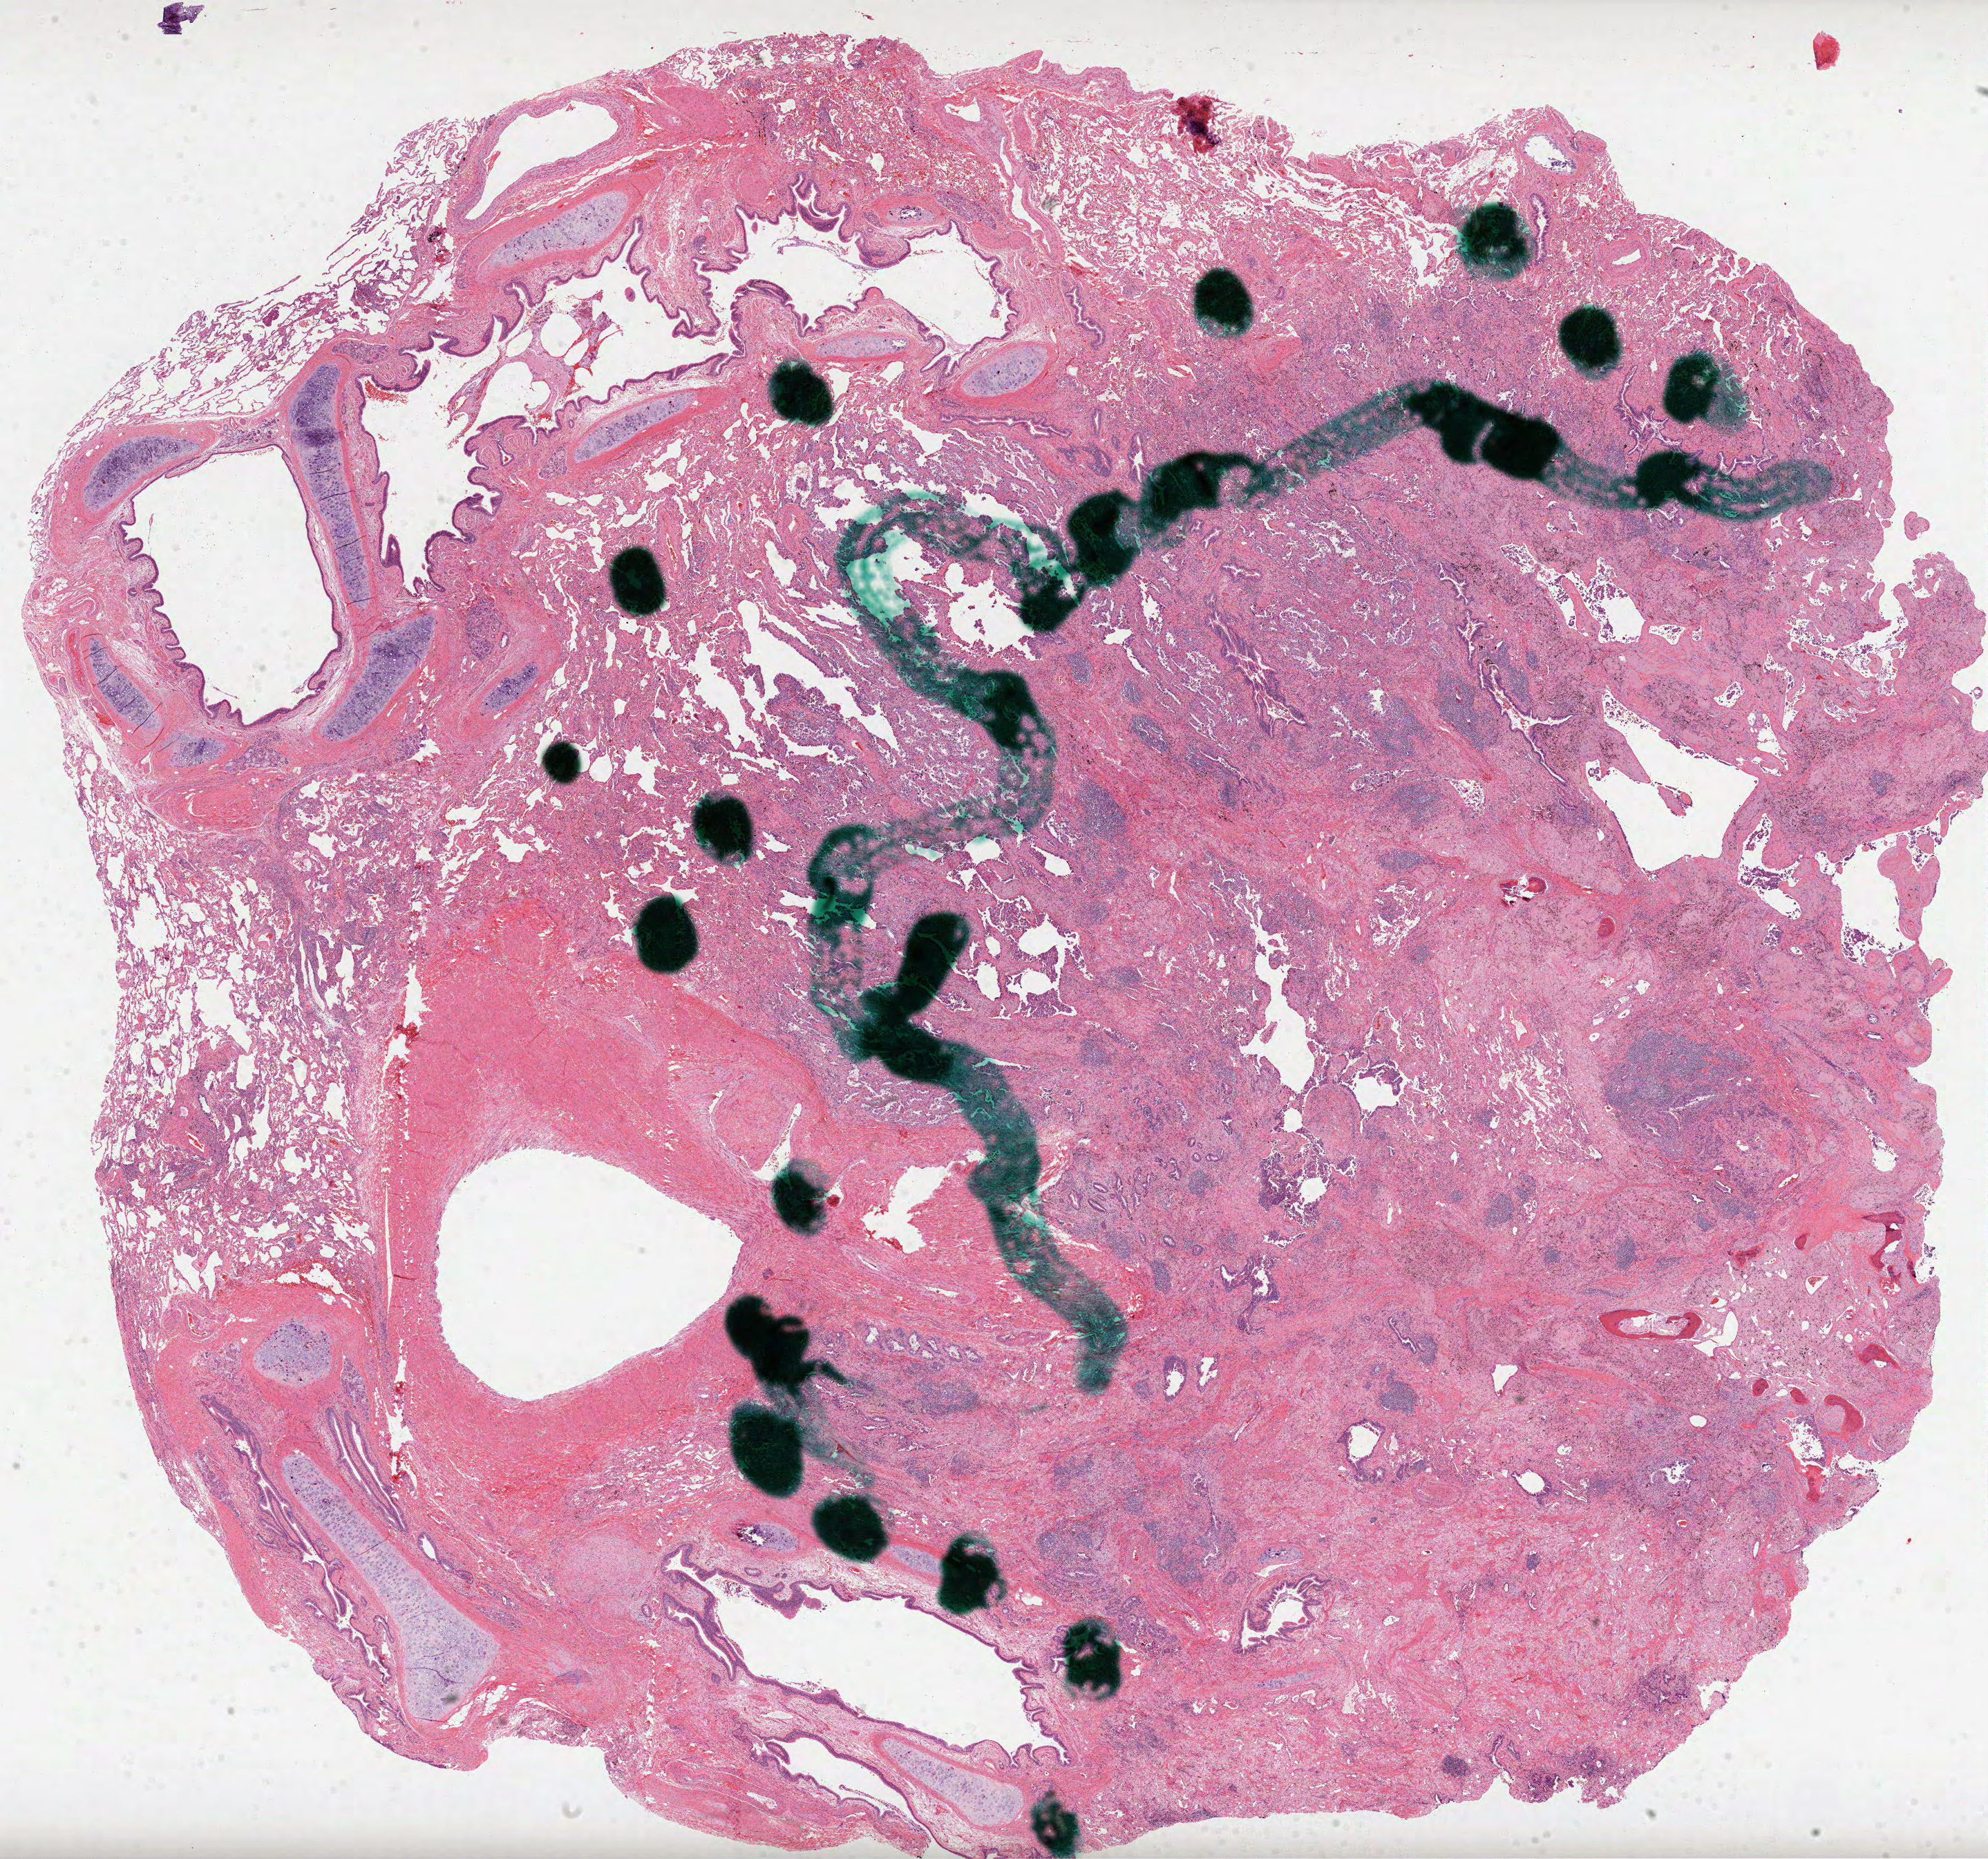
Digitized H&E-stained tissue section (whole slide), low-resolution overview of the scanned area, about 23.2 x 21.7 mm. Formalin-fixed paraffin-embedded (FFPE) diagnostic section. Lung, primary tumour sample. Female patient; age at initial diagnosis 70 years.
* histologic diagnosis: Acinar cell carcinoma (upper lobe, lung)
* AJCC pathologic stage: I
* laterality: right